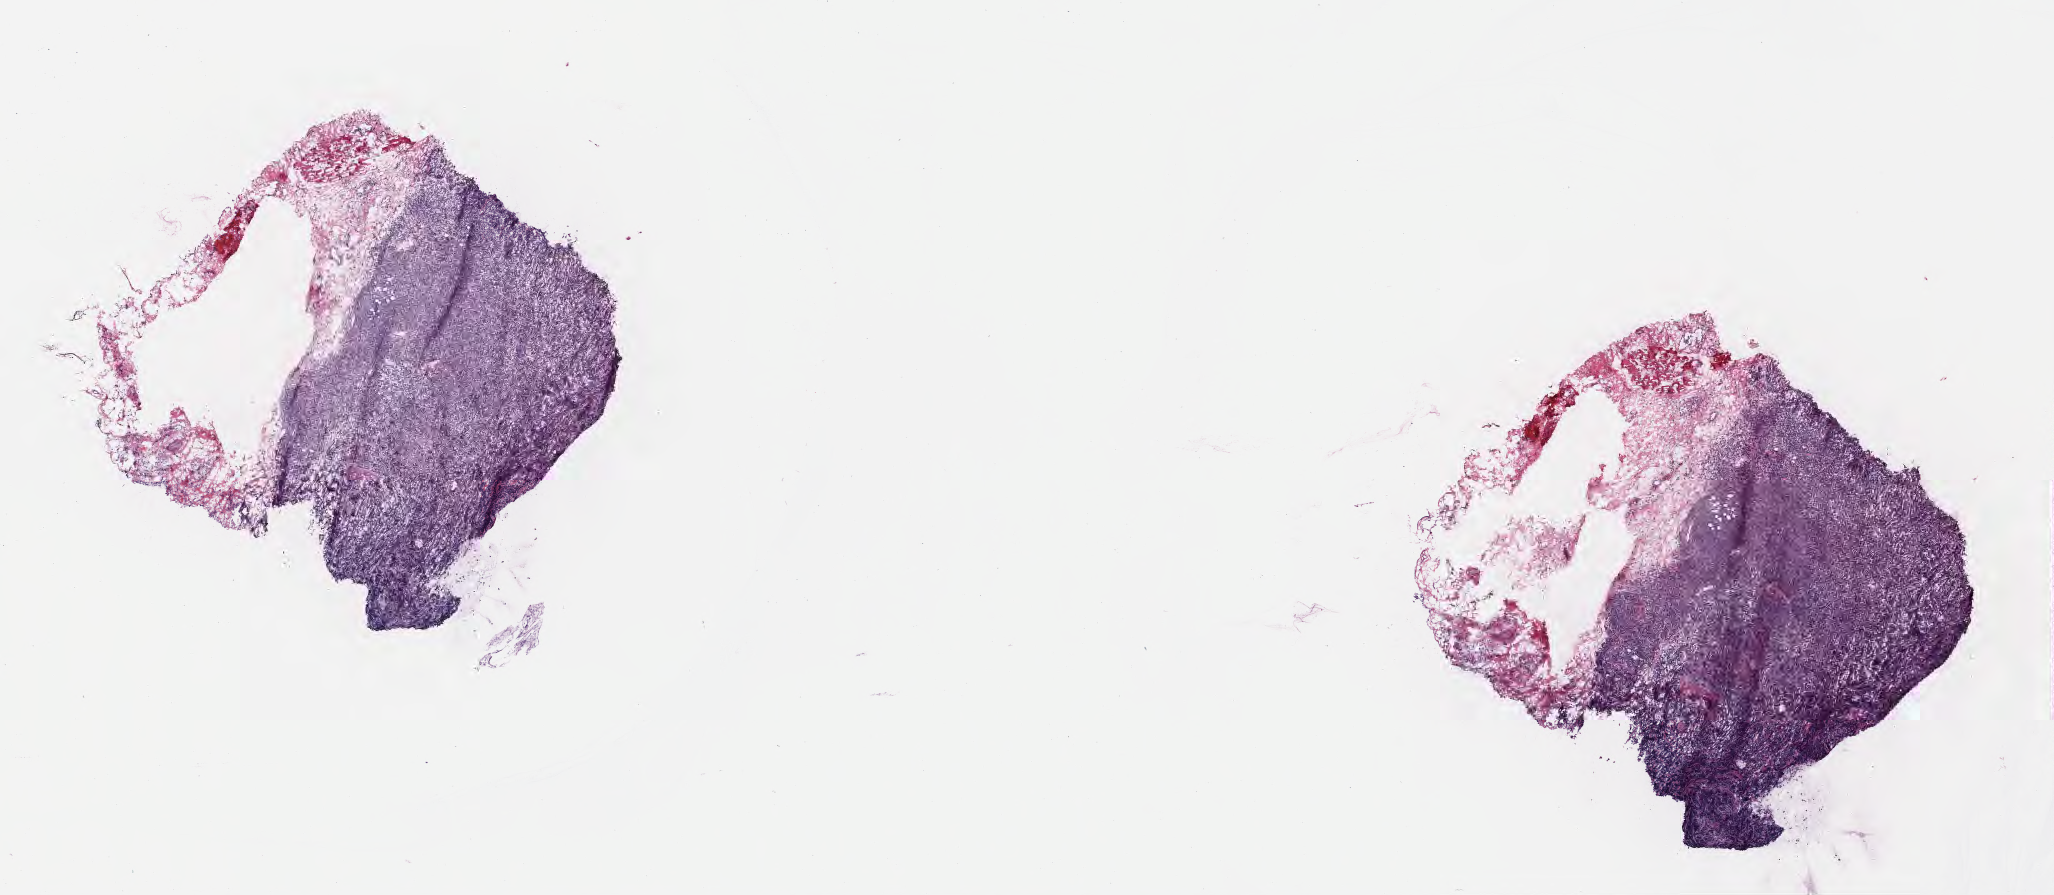
Haematoxylin and eosin whole-slide image — a low-resolution overview of the entire scanned area, about 16.6 x 7.2 mm; frozen section; primary tumor; anatomic site: cranium. Female, age 5 years at initial diagnosis. Pathologist review of this section (percent, as recorded): tumor cells 70%, tumor nuclei 90%, stromal cells 20%, necrosis 0%, normal cells 10%. Infiltration values recorded for this section: lymphocyte infiltration 40%, monocyte infiltration 30%, neutrophil infiltration 5%.
Histologic diagnosis: Burkitt lymphoma, NOS. Ann Arbor stage (patient): Stage IV.